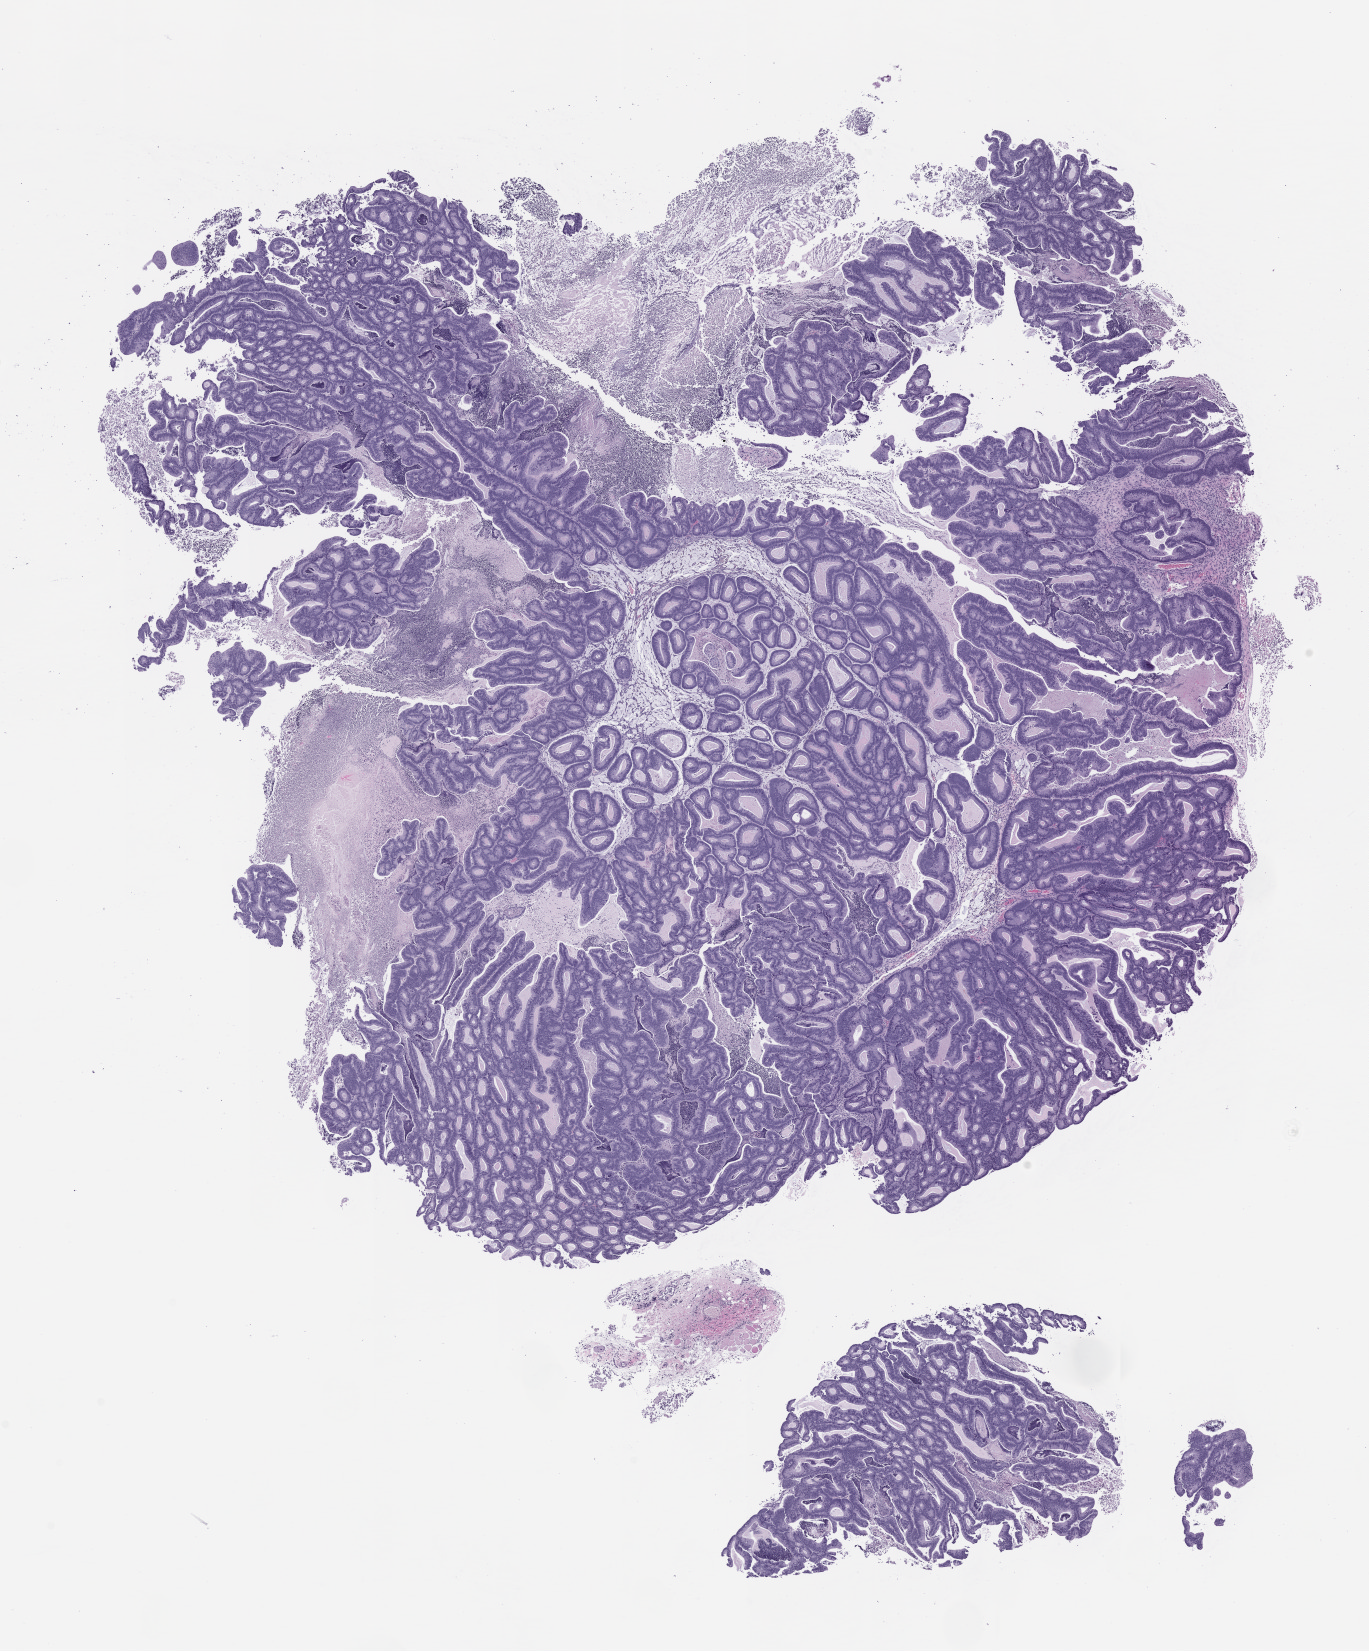
Whole-slide image, H&E: patient-derived xenograft (human tumor grown in a mouse), passage 1, shown as a low-resolution overview of the whole scanned area (about 11.0 x 13.3 mm); formalin-fixed paraffin-embedded section; originating tumor site category: colon.
Originating patient diagnosis: Colon Adenocarcinoma.